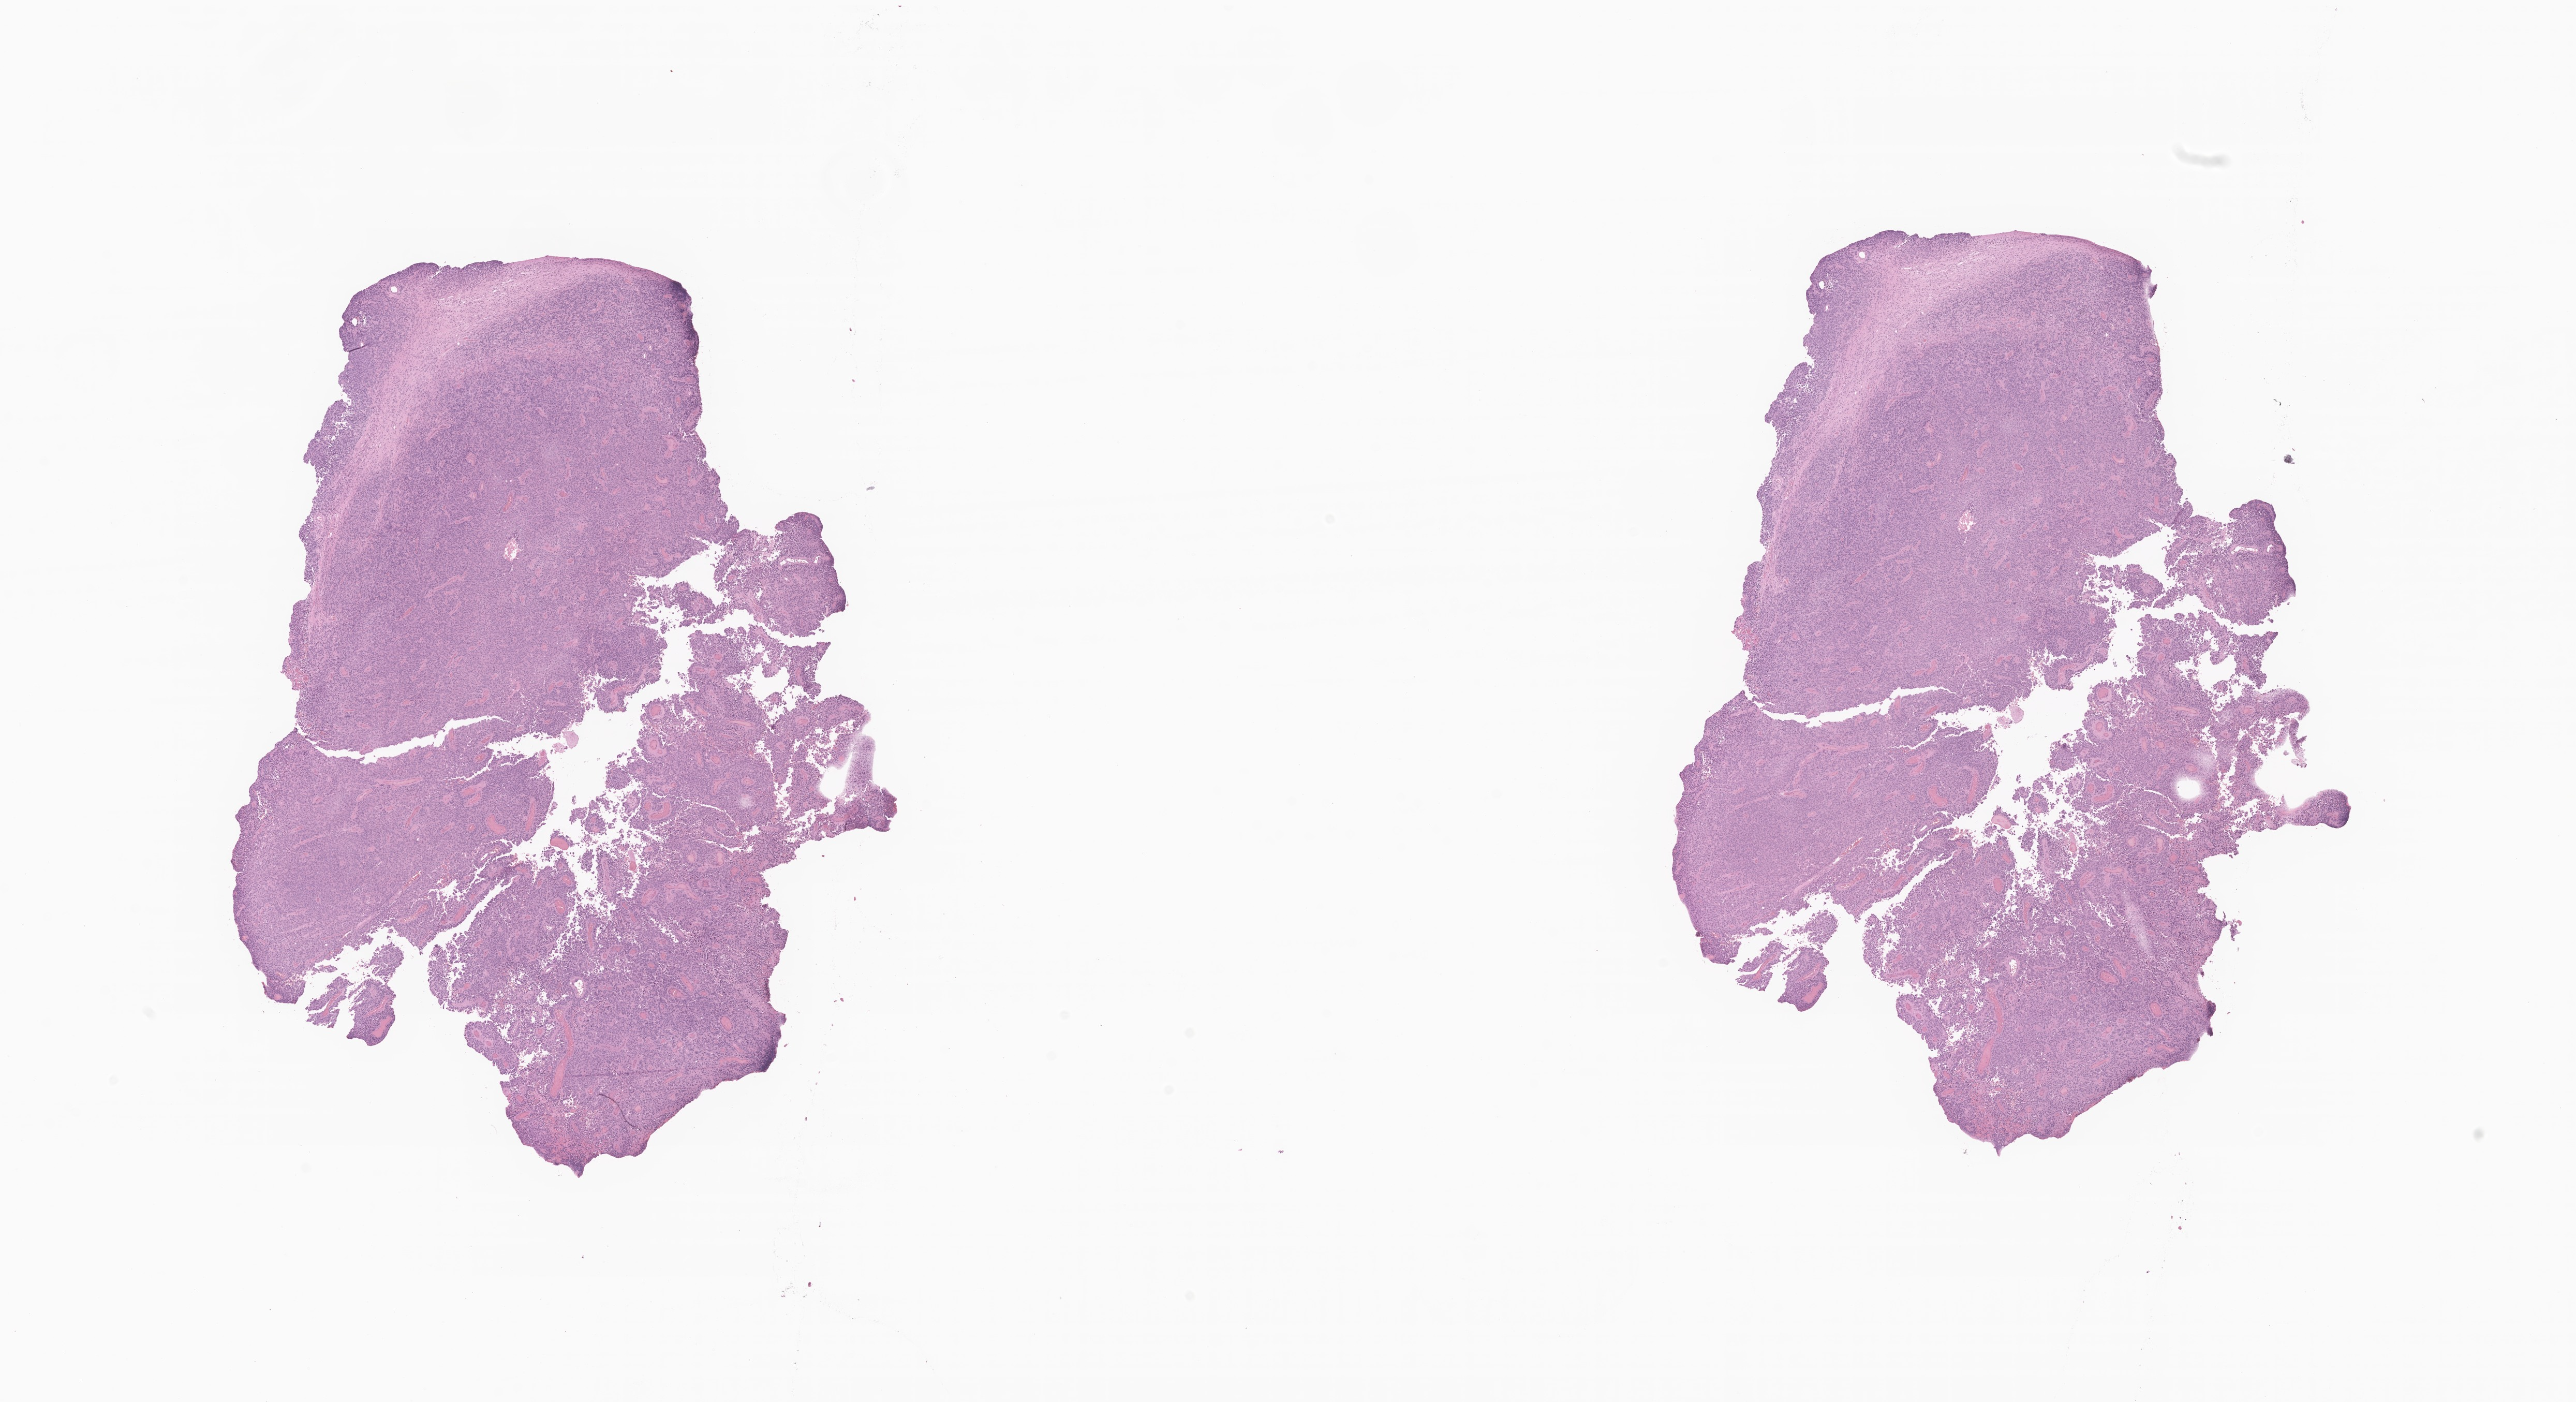
Digitized hematoxylin and eosin (H&E)-stained section of tumor tissue from the pineal gland, low-resolution overview of the scanned area, about 21.0 x 11.4 mm; FFPE section. Patient: male, age 212 months (17 years 8 months).
• recorded diagnosis: Pinealoma